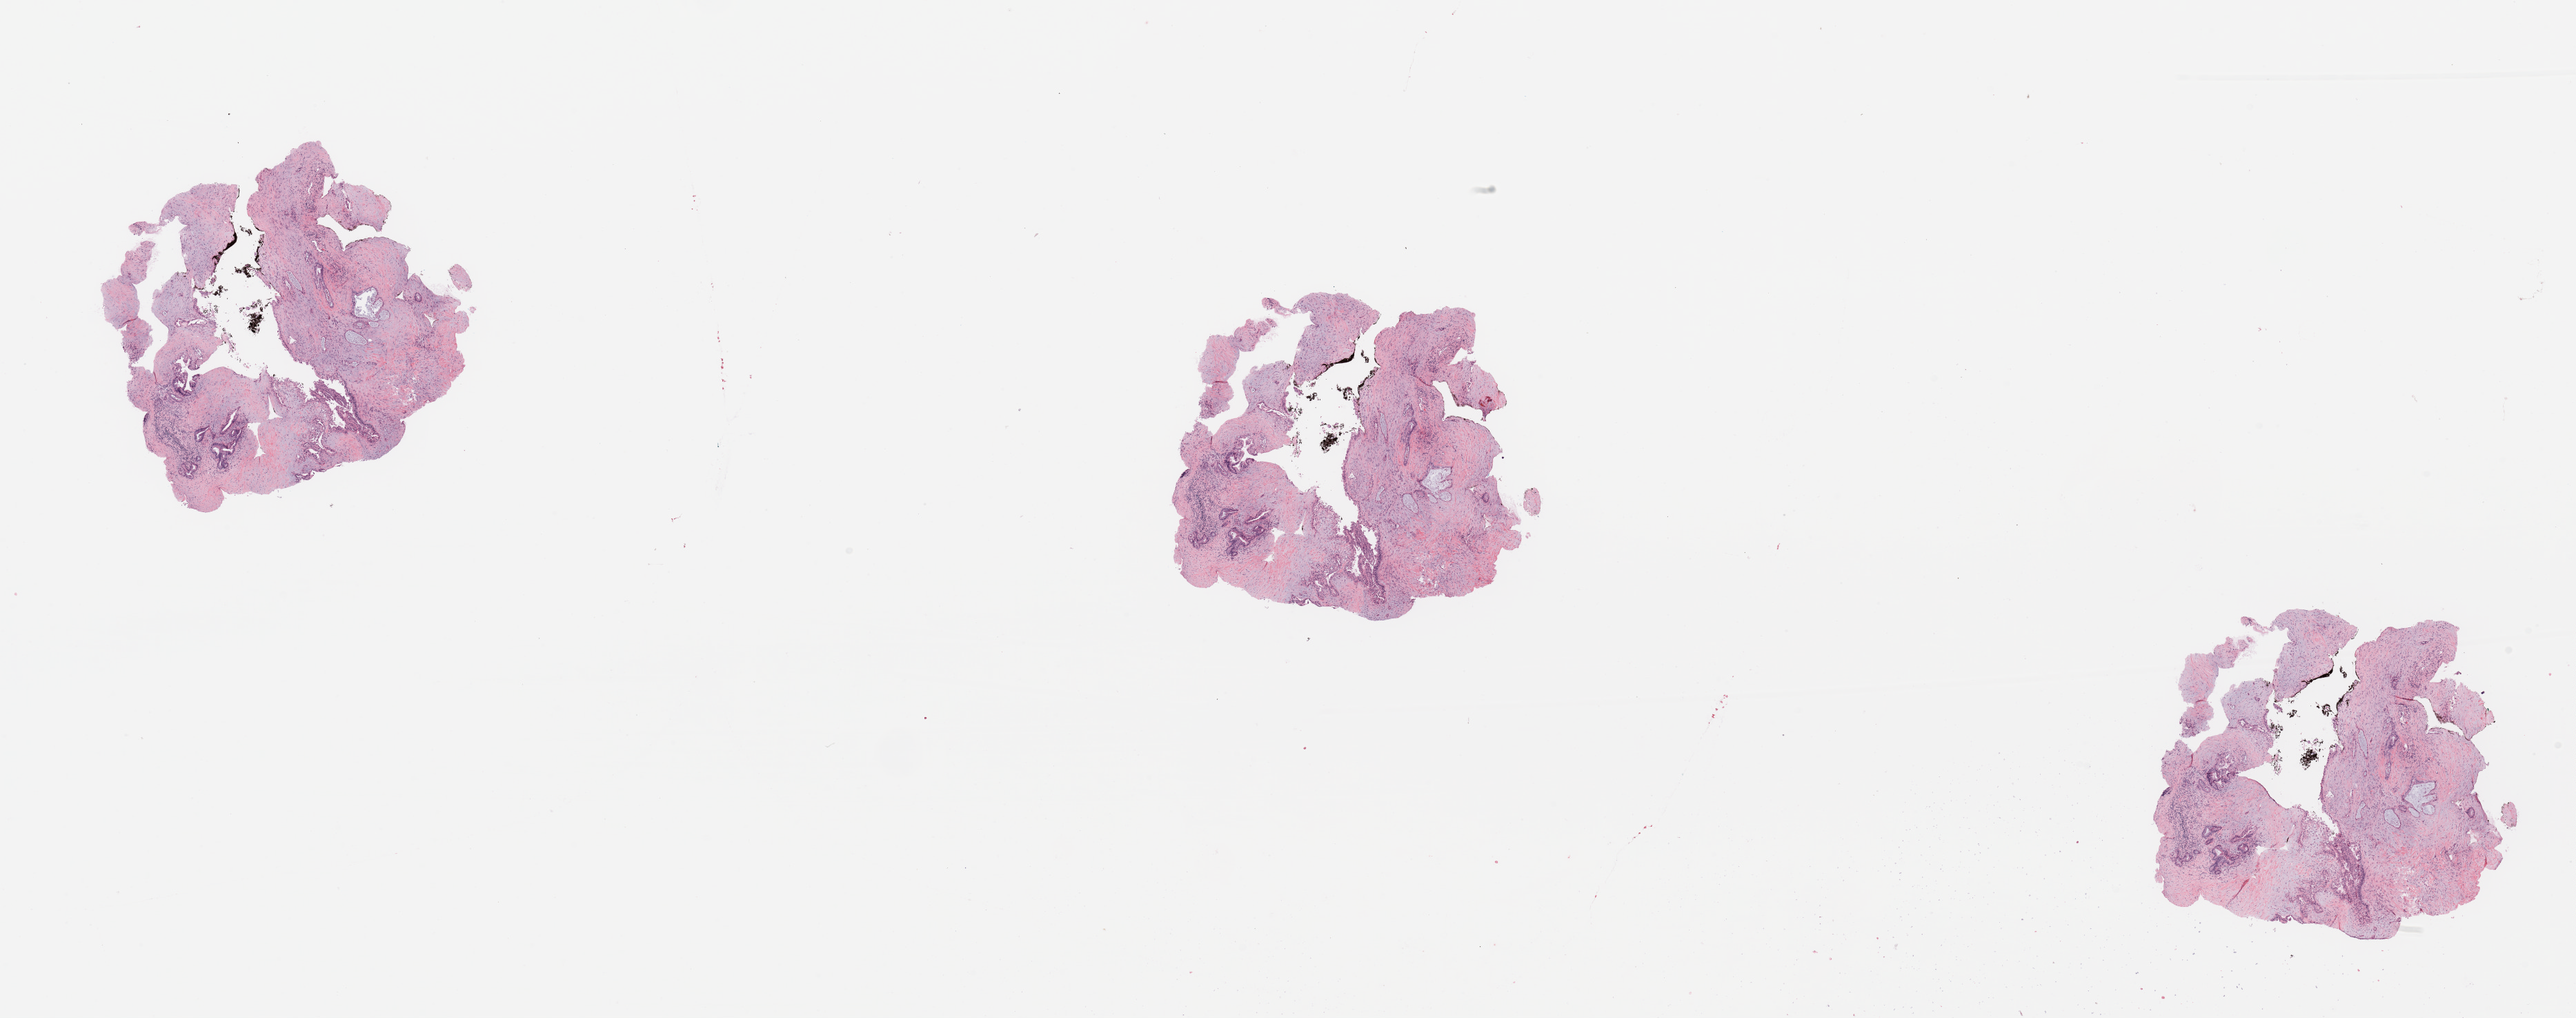
Digitized H&E tissue section (whole slide) — shown as a low-resolution overview of the whole scanned area (about 29.5 x 11.7 mm, acquisition: 20x scan); tumour tissue sample, pancreas. 79-year-old female patient. Histologic grade: G2 (moderately differentiated).
Primary tumour site (as recorded): body. AJCC pathologic stage: III. Histologic diagnosis: Infiltrating duct carcinoma, NOS.